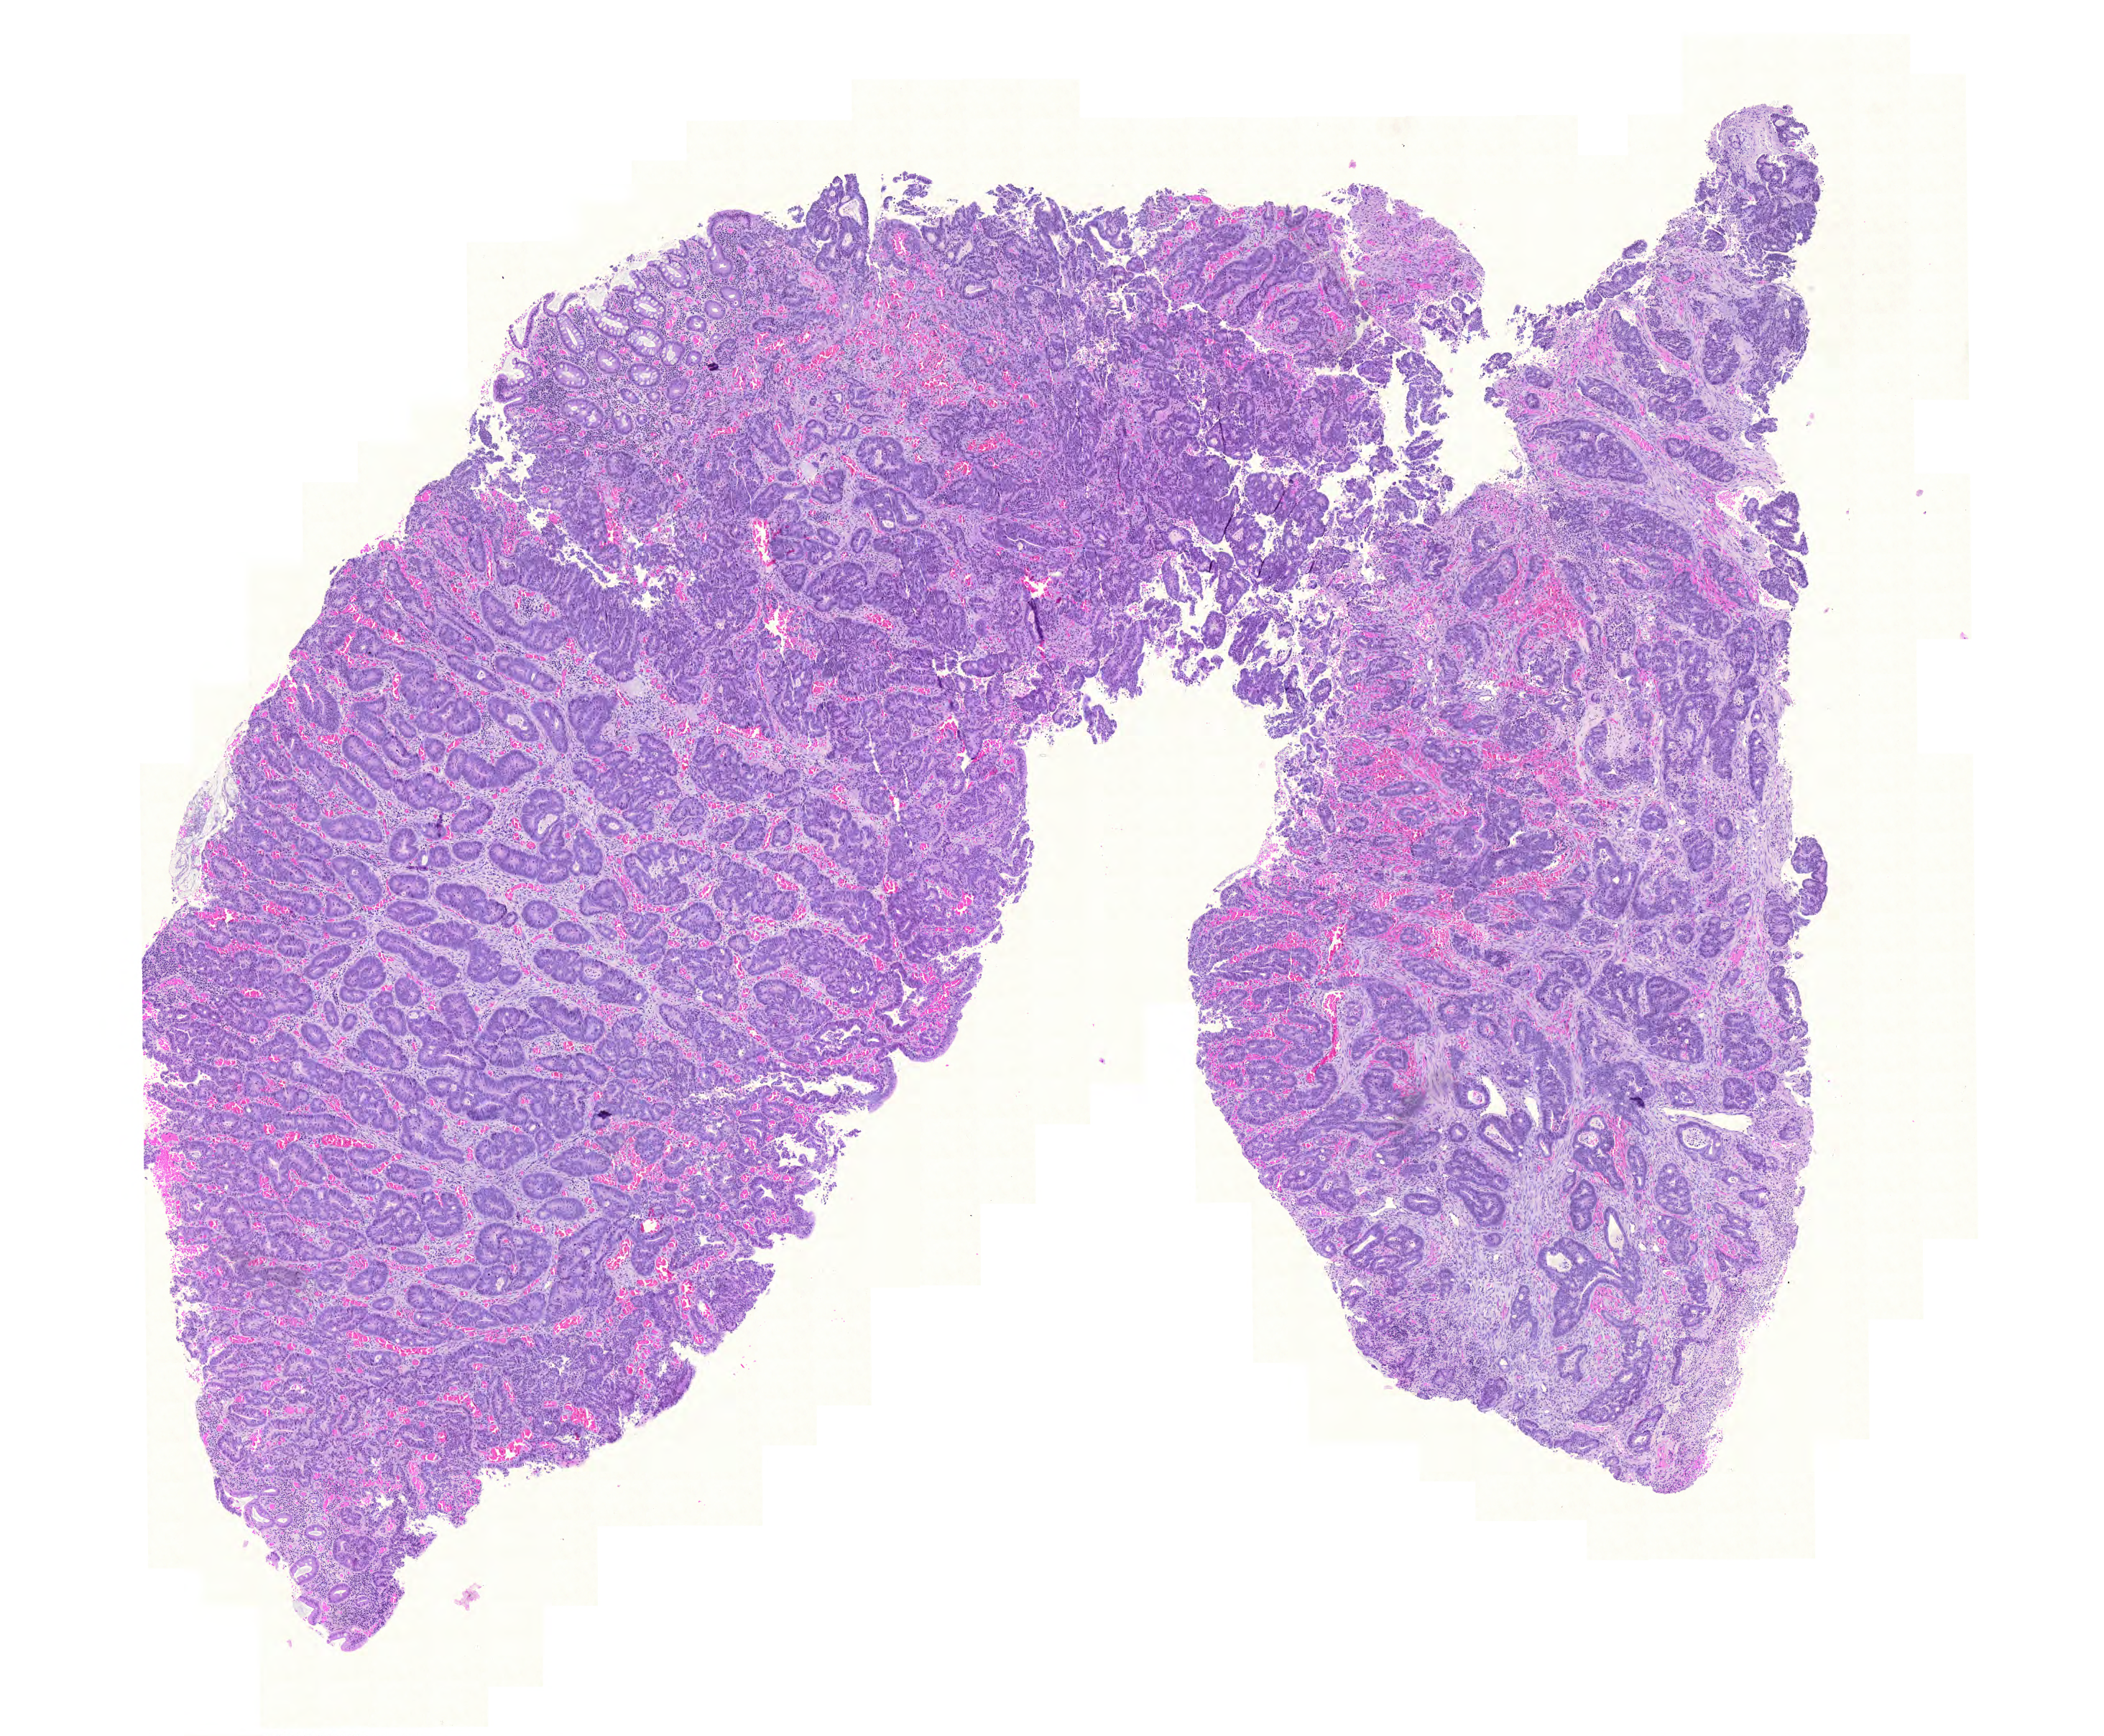
Whole-slide histology image, H&E-stained, low-resolution overview of the scanned area, about 10.9 x 9.0 mm. Formalin-fixed paraffin-embedded (FFPE) diagnostic section. Primary tumour sample from the colon. Female, age 53 years at initial diagnosis.
Histologic diagnosis: Adenocarcinoma, NOS (sigmoid colon). Lymph nodes positive (case pathology): 2 of 14 examined. AJCC pathologic stage: IIIB (6th edition).